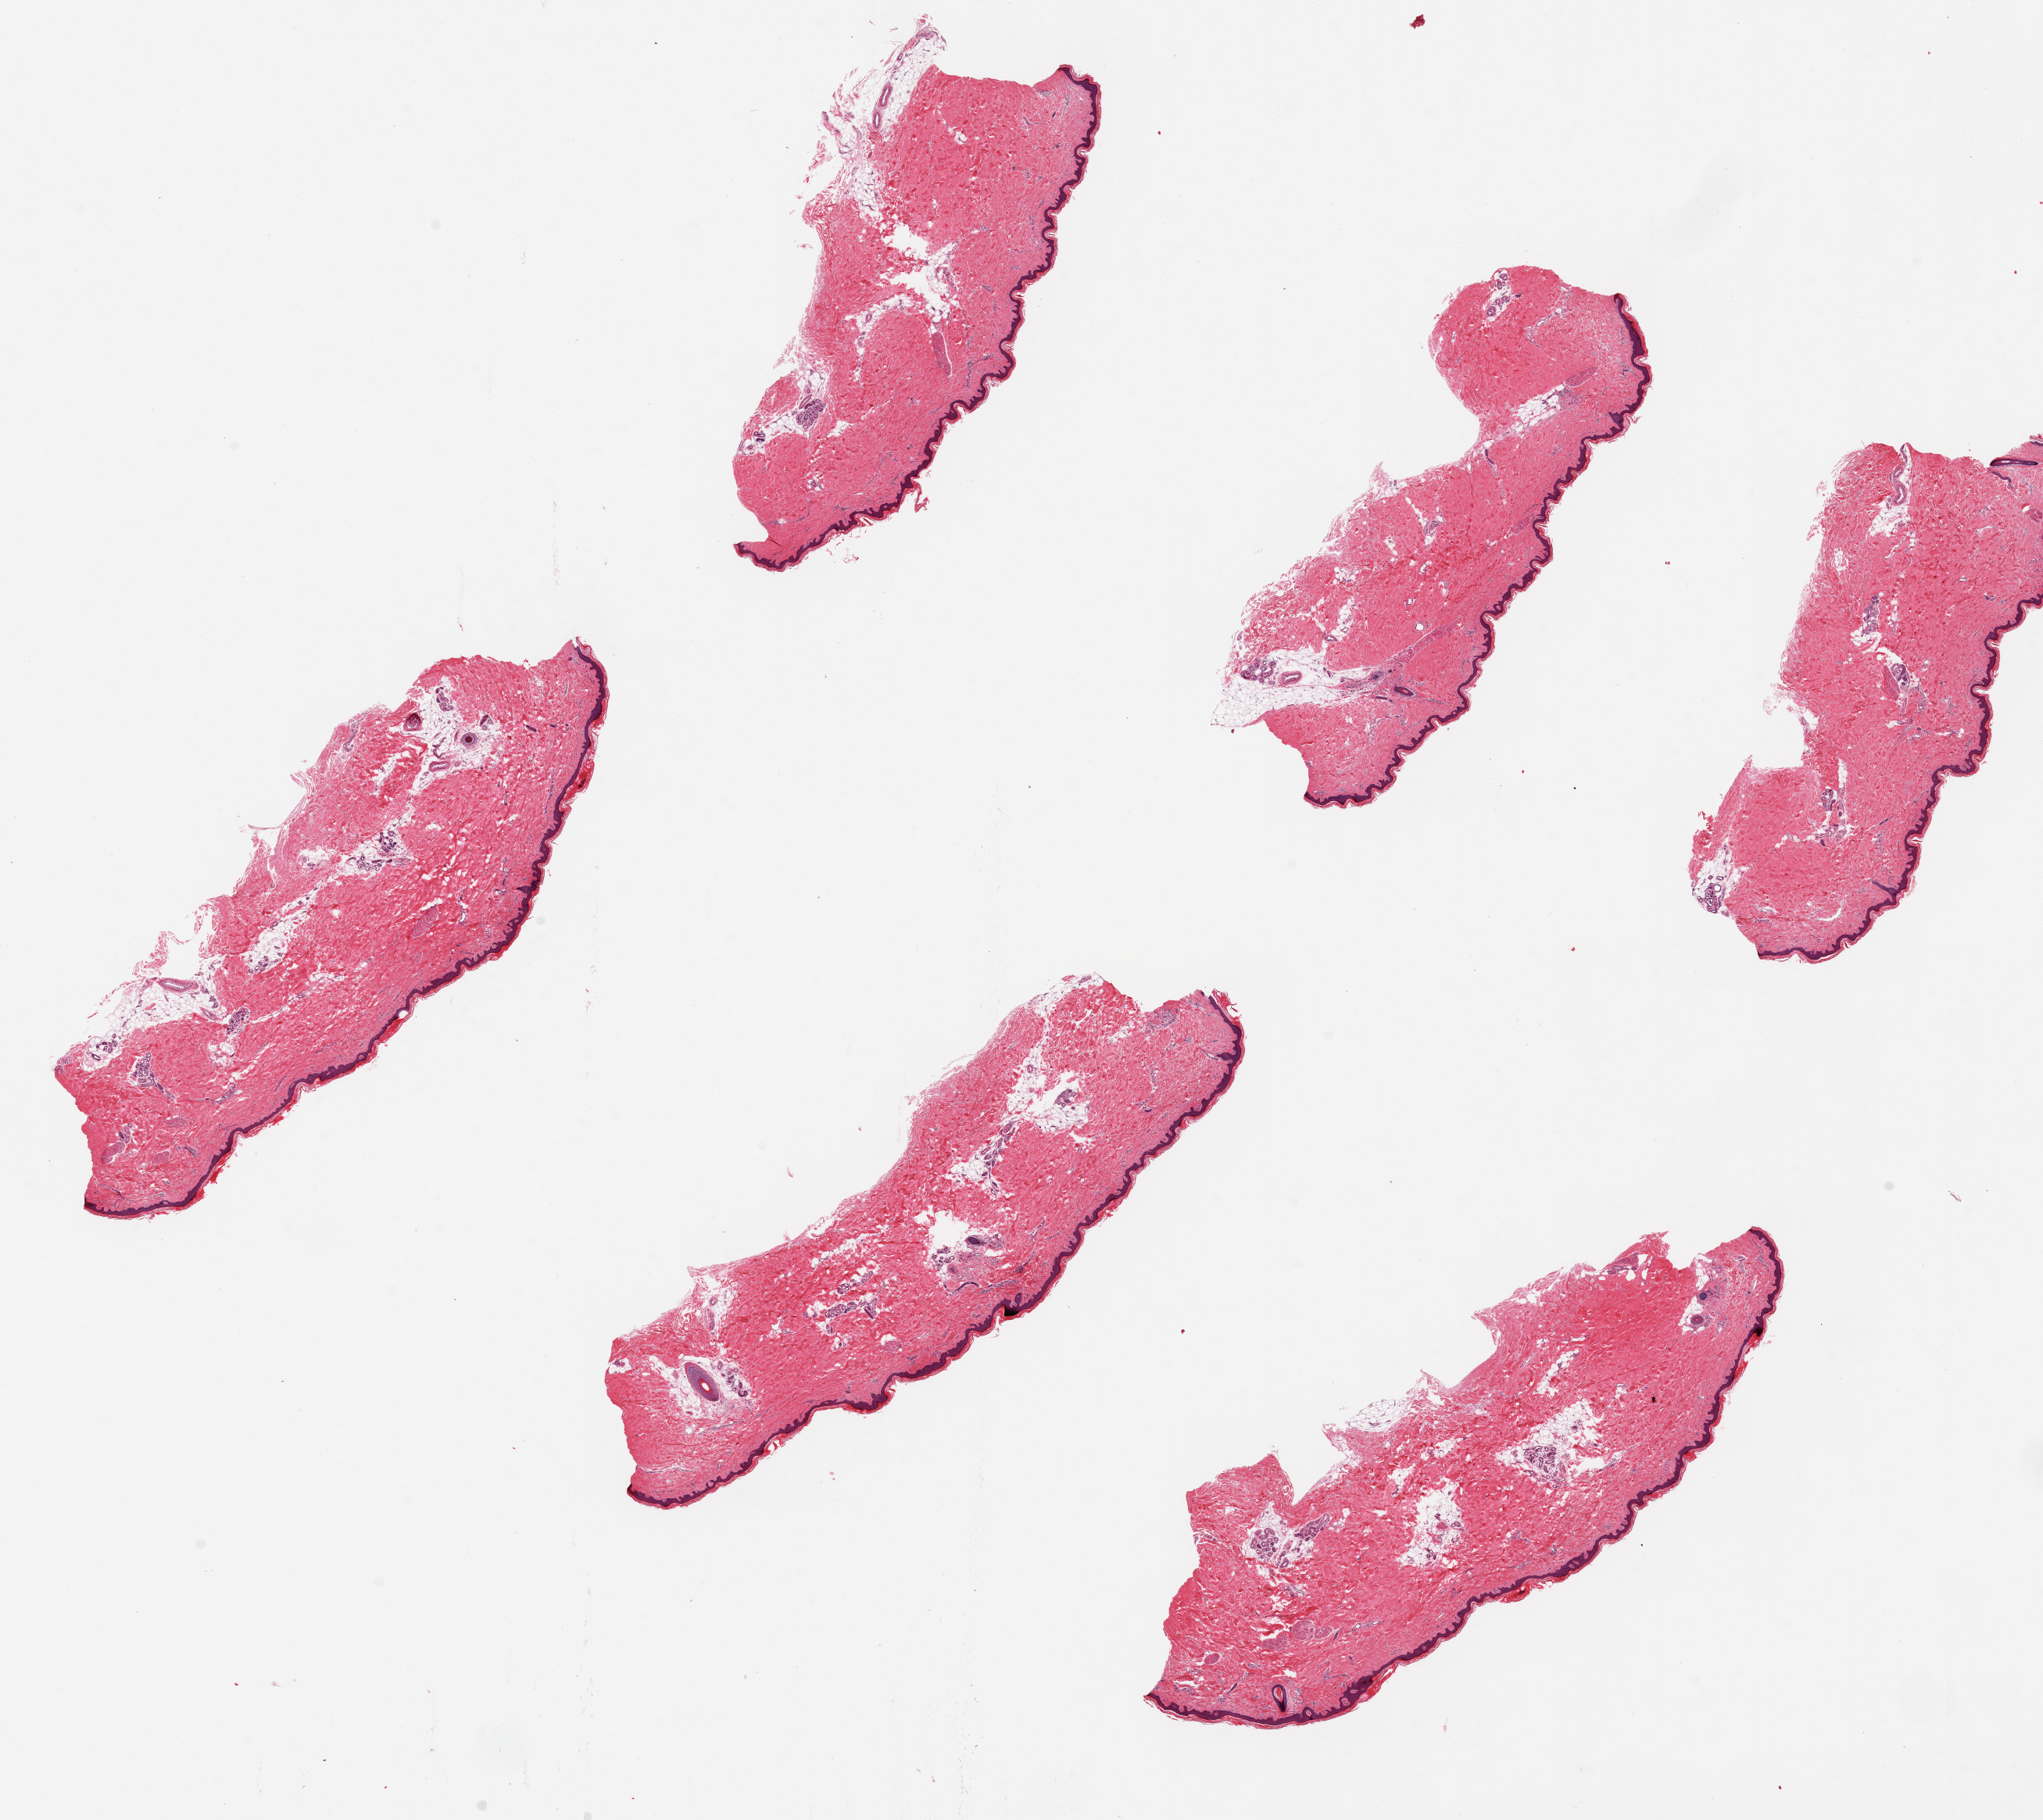
Haematoxylin and eosin whole-slide image — low-resolution overview of the scanned area, about 20.7 x 18.4 mm (from a 20x scan); PAXgene-fixed, paraffin-embedded tissue; sampled site (target tissue): skin of lower leg; donor tissue sample. Donor: female.
• reviewer comment on this tissue sample: 6 pieces ~6x2.5mm; squamous epithelium is ~2-3% of thickness